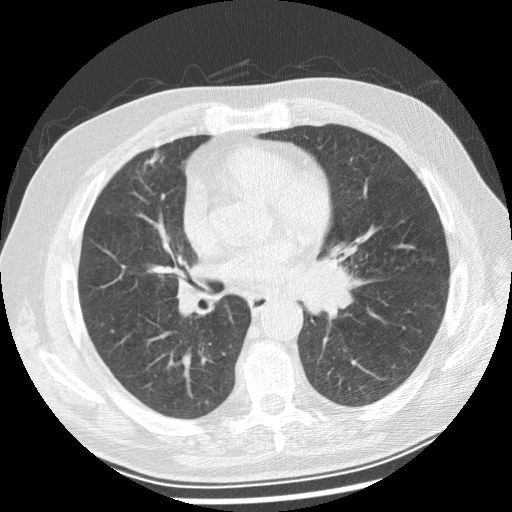
Chest CT (low-dose screening protocol), one axial image; baseline annual screen; lung window (W 1500 / L -600 HU); 2.5 mm slice thickness; 512 × 512 image matrix, field of view 360 × 360 mm. Male participant, aged 70 years at enrolment.
- Lesion marked by an expert reader, bounding box <292,240,376,323> (left, top, right, bottom; pixels).
- Screening reader's record for this exam: no non-calcified nodule ≥4 mm recorded.
- Lung cancer was diagnosed 29 days after this screen: squamous cell carcinoma, keratinizing, NOS, left main stem bronchus, moderately differentiated (G2), stage IIIB (AJCC 6th edition), 40 mm at pathology.